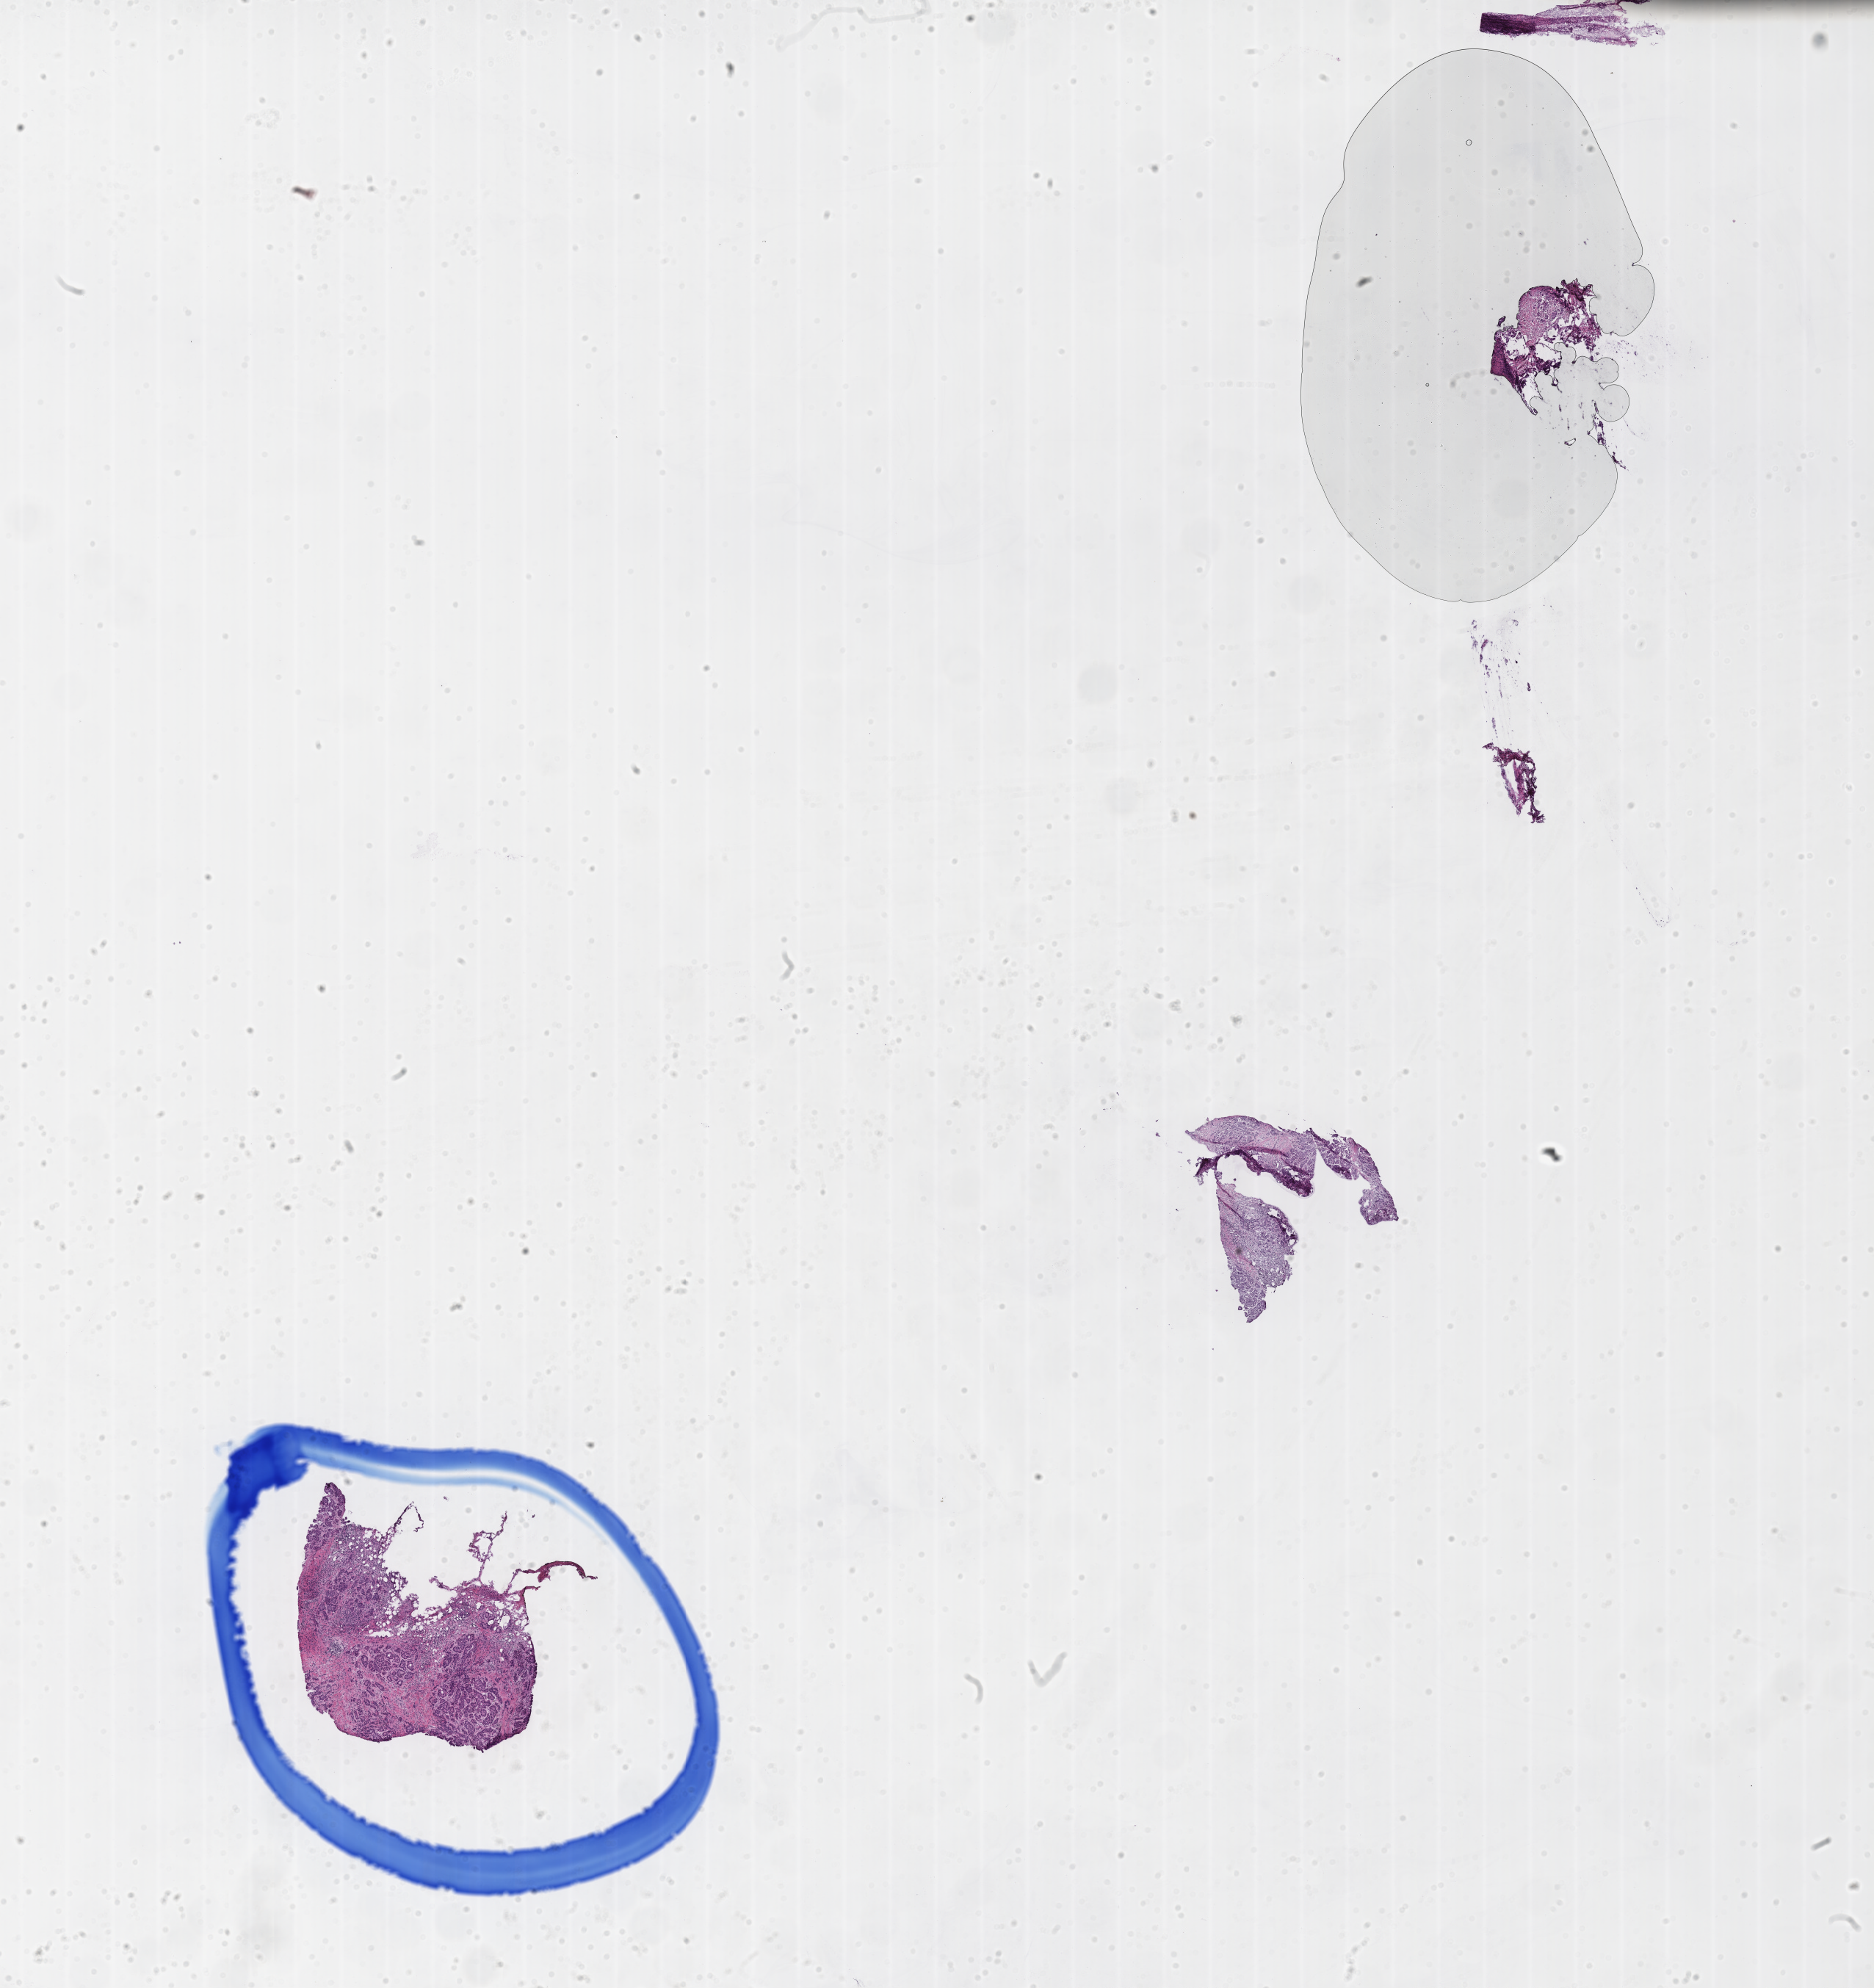
Whole-slide image, H&E stain, whole scanned area (about 20.6 x 21.8 mm) shown as a low-resolution overview; frozen section (tissue freezing medium); primary tumor; site: breast (left). Female patient; age at initial diagnosis 79 years. Slide review estimates, as recorded: tumor cells 80%, tumor nuclei 80%, stromal cells 20%, necrosis 0%, normal cells 0%. Infiltration values recorded for this section: lymphocyte infiltration 8%, monocyte infiltration 2%, neutrophil infiltration 5%.
Histologic diagnosis: Infiltrating duct carcinoma, NOS. Section: bottom of the tissue portion.